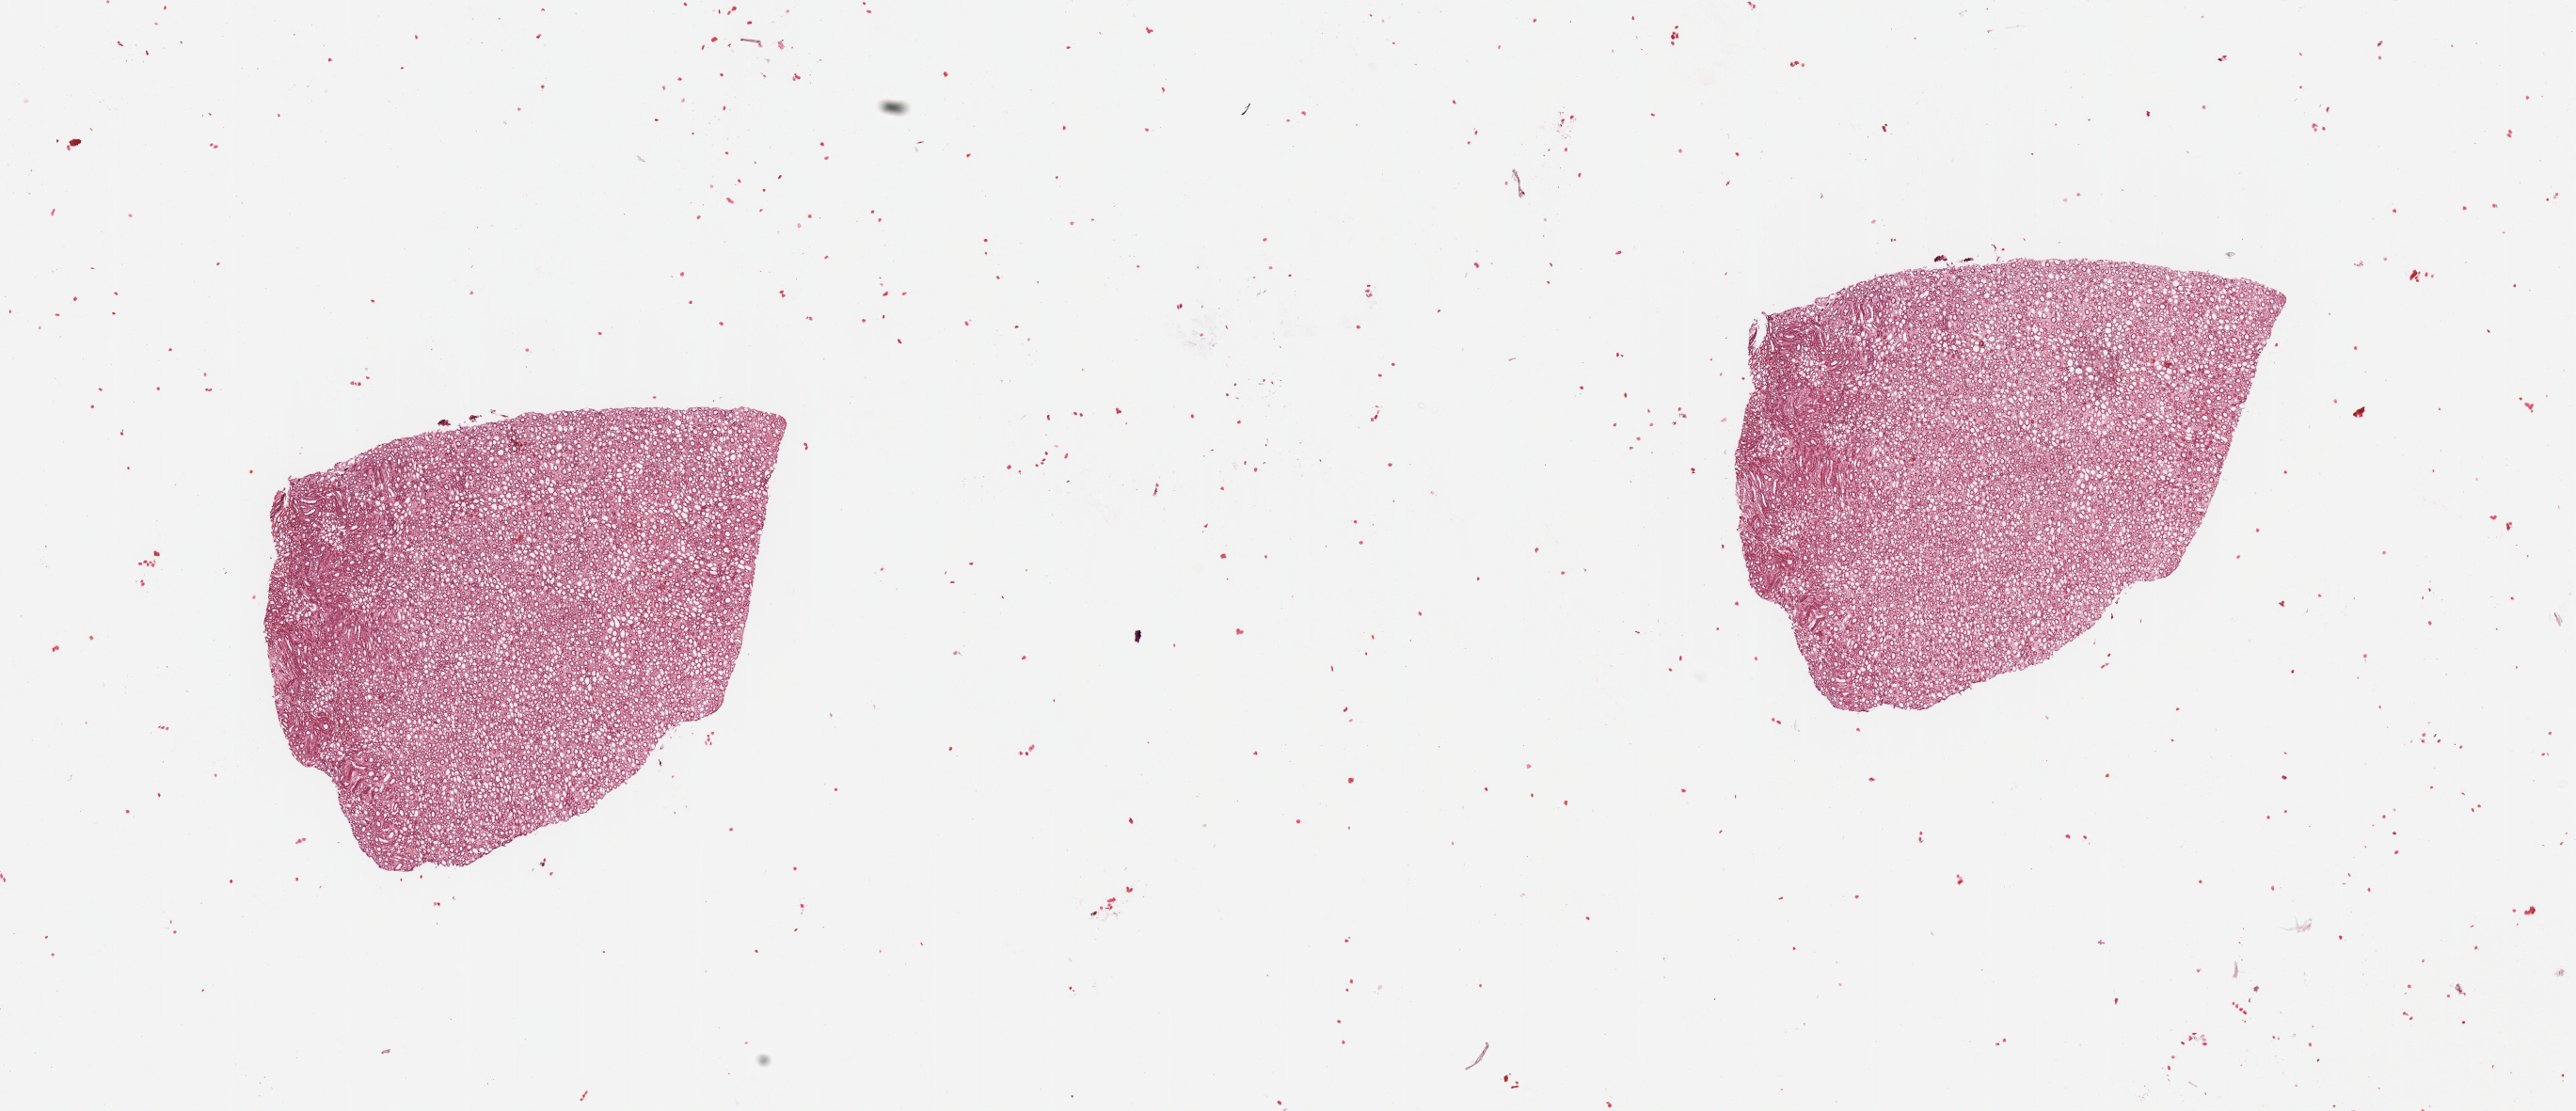
Whole-slide histology image, H&E-stained — a low-resolution overview of the entire scanned area, about 21.7 x 9.3 mm (acquisition: 20x scan). Normal (non-tumour) tissue sample, sampled site: kidney. Female, 60 y/o.
This section: normal (non-tumour) tissue from the same patient. Patient diagnosis: Renal cell carcinoma, NOS.